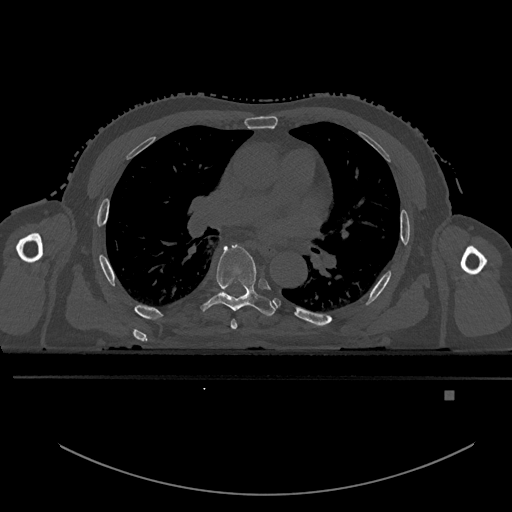
CT including the spine, one axial slice; position 312 of 969 along the scan axis; bone window (W 1800 / L 400 HU); 0.5 mm slice thickness; 512 × 512 image matrix, field of view 456 × 456 mm. Male patient, age 82 years. From the clinical record (not read from this slice): primary cancer: prostate.
Structures marked on this image (semi-automatically segmented with operator editing):
- T5 vertebra: box from (x=230, y=320) to (x=237, y=330) px
- T6 vertebra: (x=200, y=244)–(x=277, y=317)